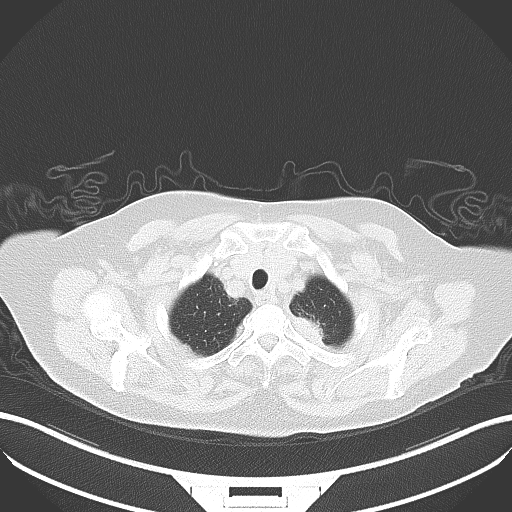
Chest CT, one axial slice. Position 44 of 50 along the scan axis. 100 kVp. Lung window (W 1500 / L -600 HU). 5 mm slice thickness. 512 × 512 image matrix. Patient: female, 81 years. From the clinical record (not read from this slice): clinical TNM (as recorded): T2a N0 M0.
Annotated regions visible in this slice (rectangle marked by the reading radiologist):
- lung tumour (recorded histology: adenocarcinoma): bounding box [x1, y1, x2, y2] px = [295, 311, 328, 345]